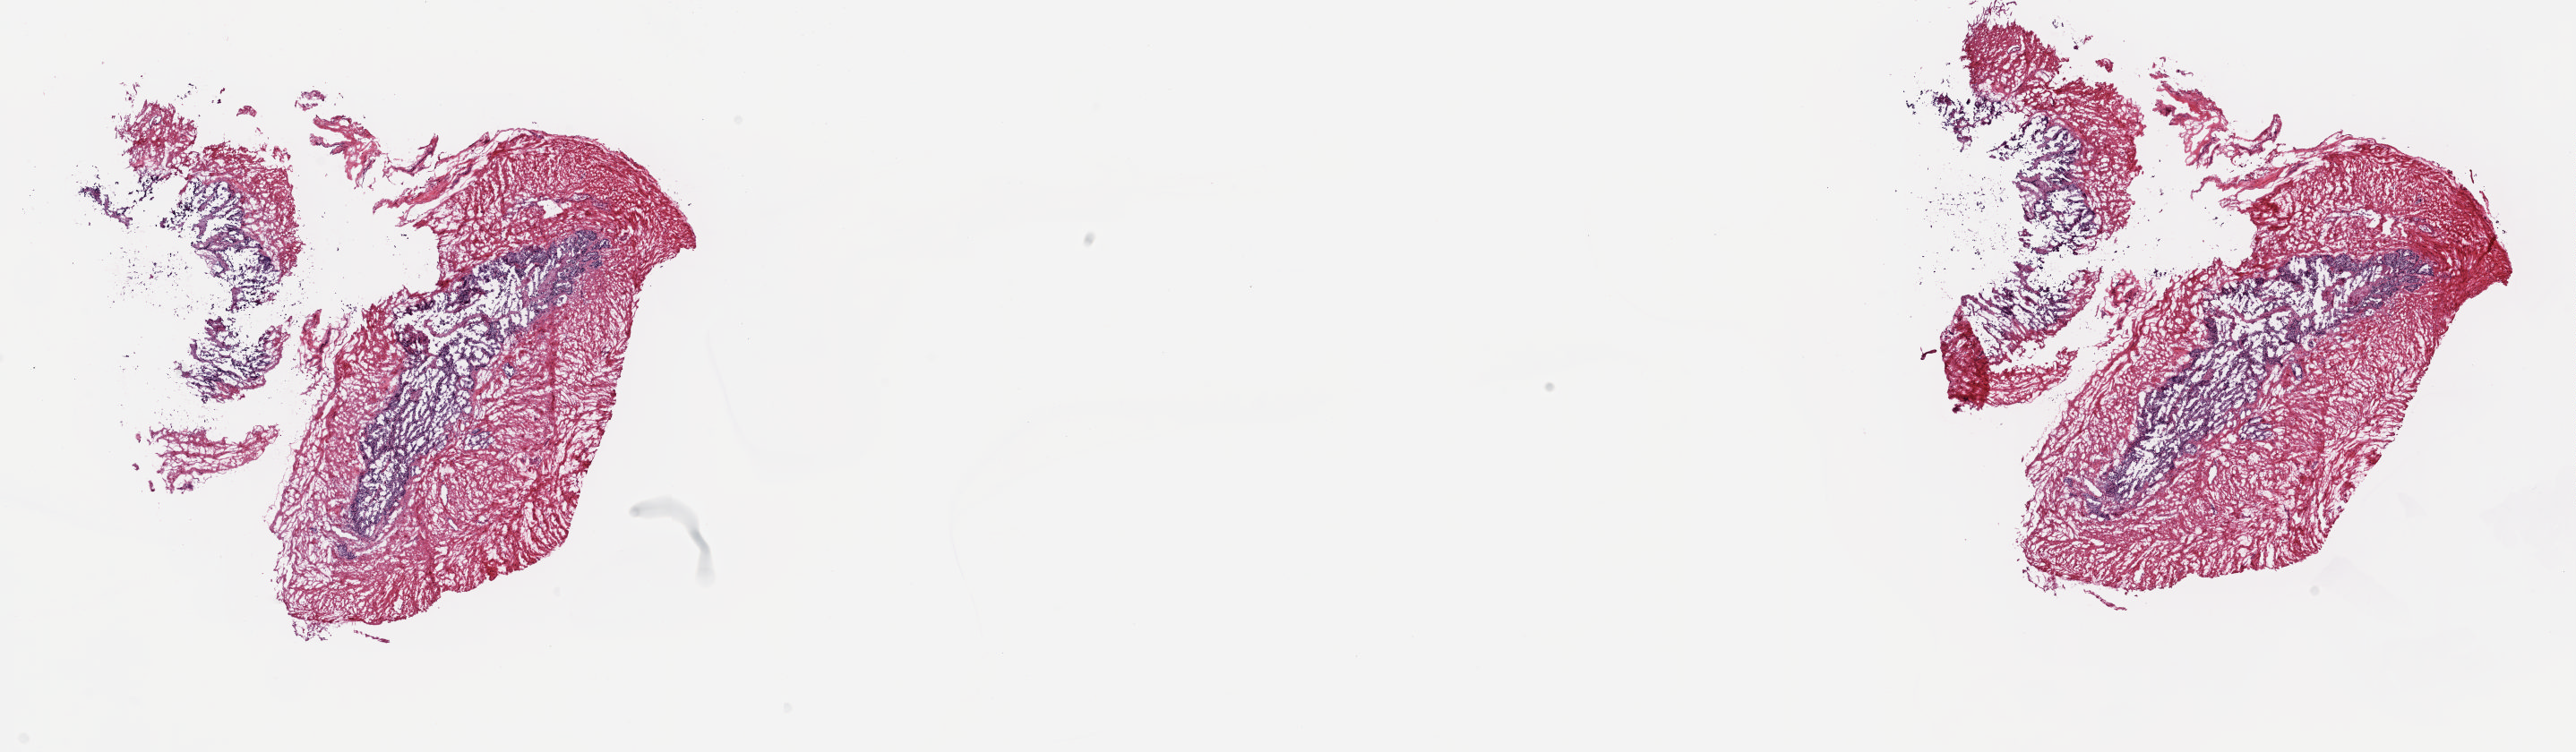
Digitized Hematoxylin and eosin (H&E) stained tissue section (whole slide), shown as a low-resolution overview of the whole scanned area (about 22.8 x 6.7 mm). Frozen section. Solid tissue normal (non-tumour tissue) sample from the prostate. Male, age 67 years at initial diagnosis. Composition of this section per pathologist review: tumour cells 0%, tumour nuclei 0%.
This section: solid tissue normal (non-tumour) sample from the same patient. Patient diagnosis: Adenocarcinoma, NOS (prostate gland).